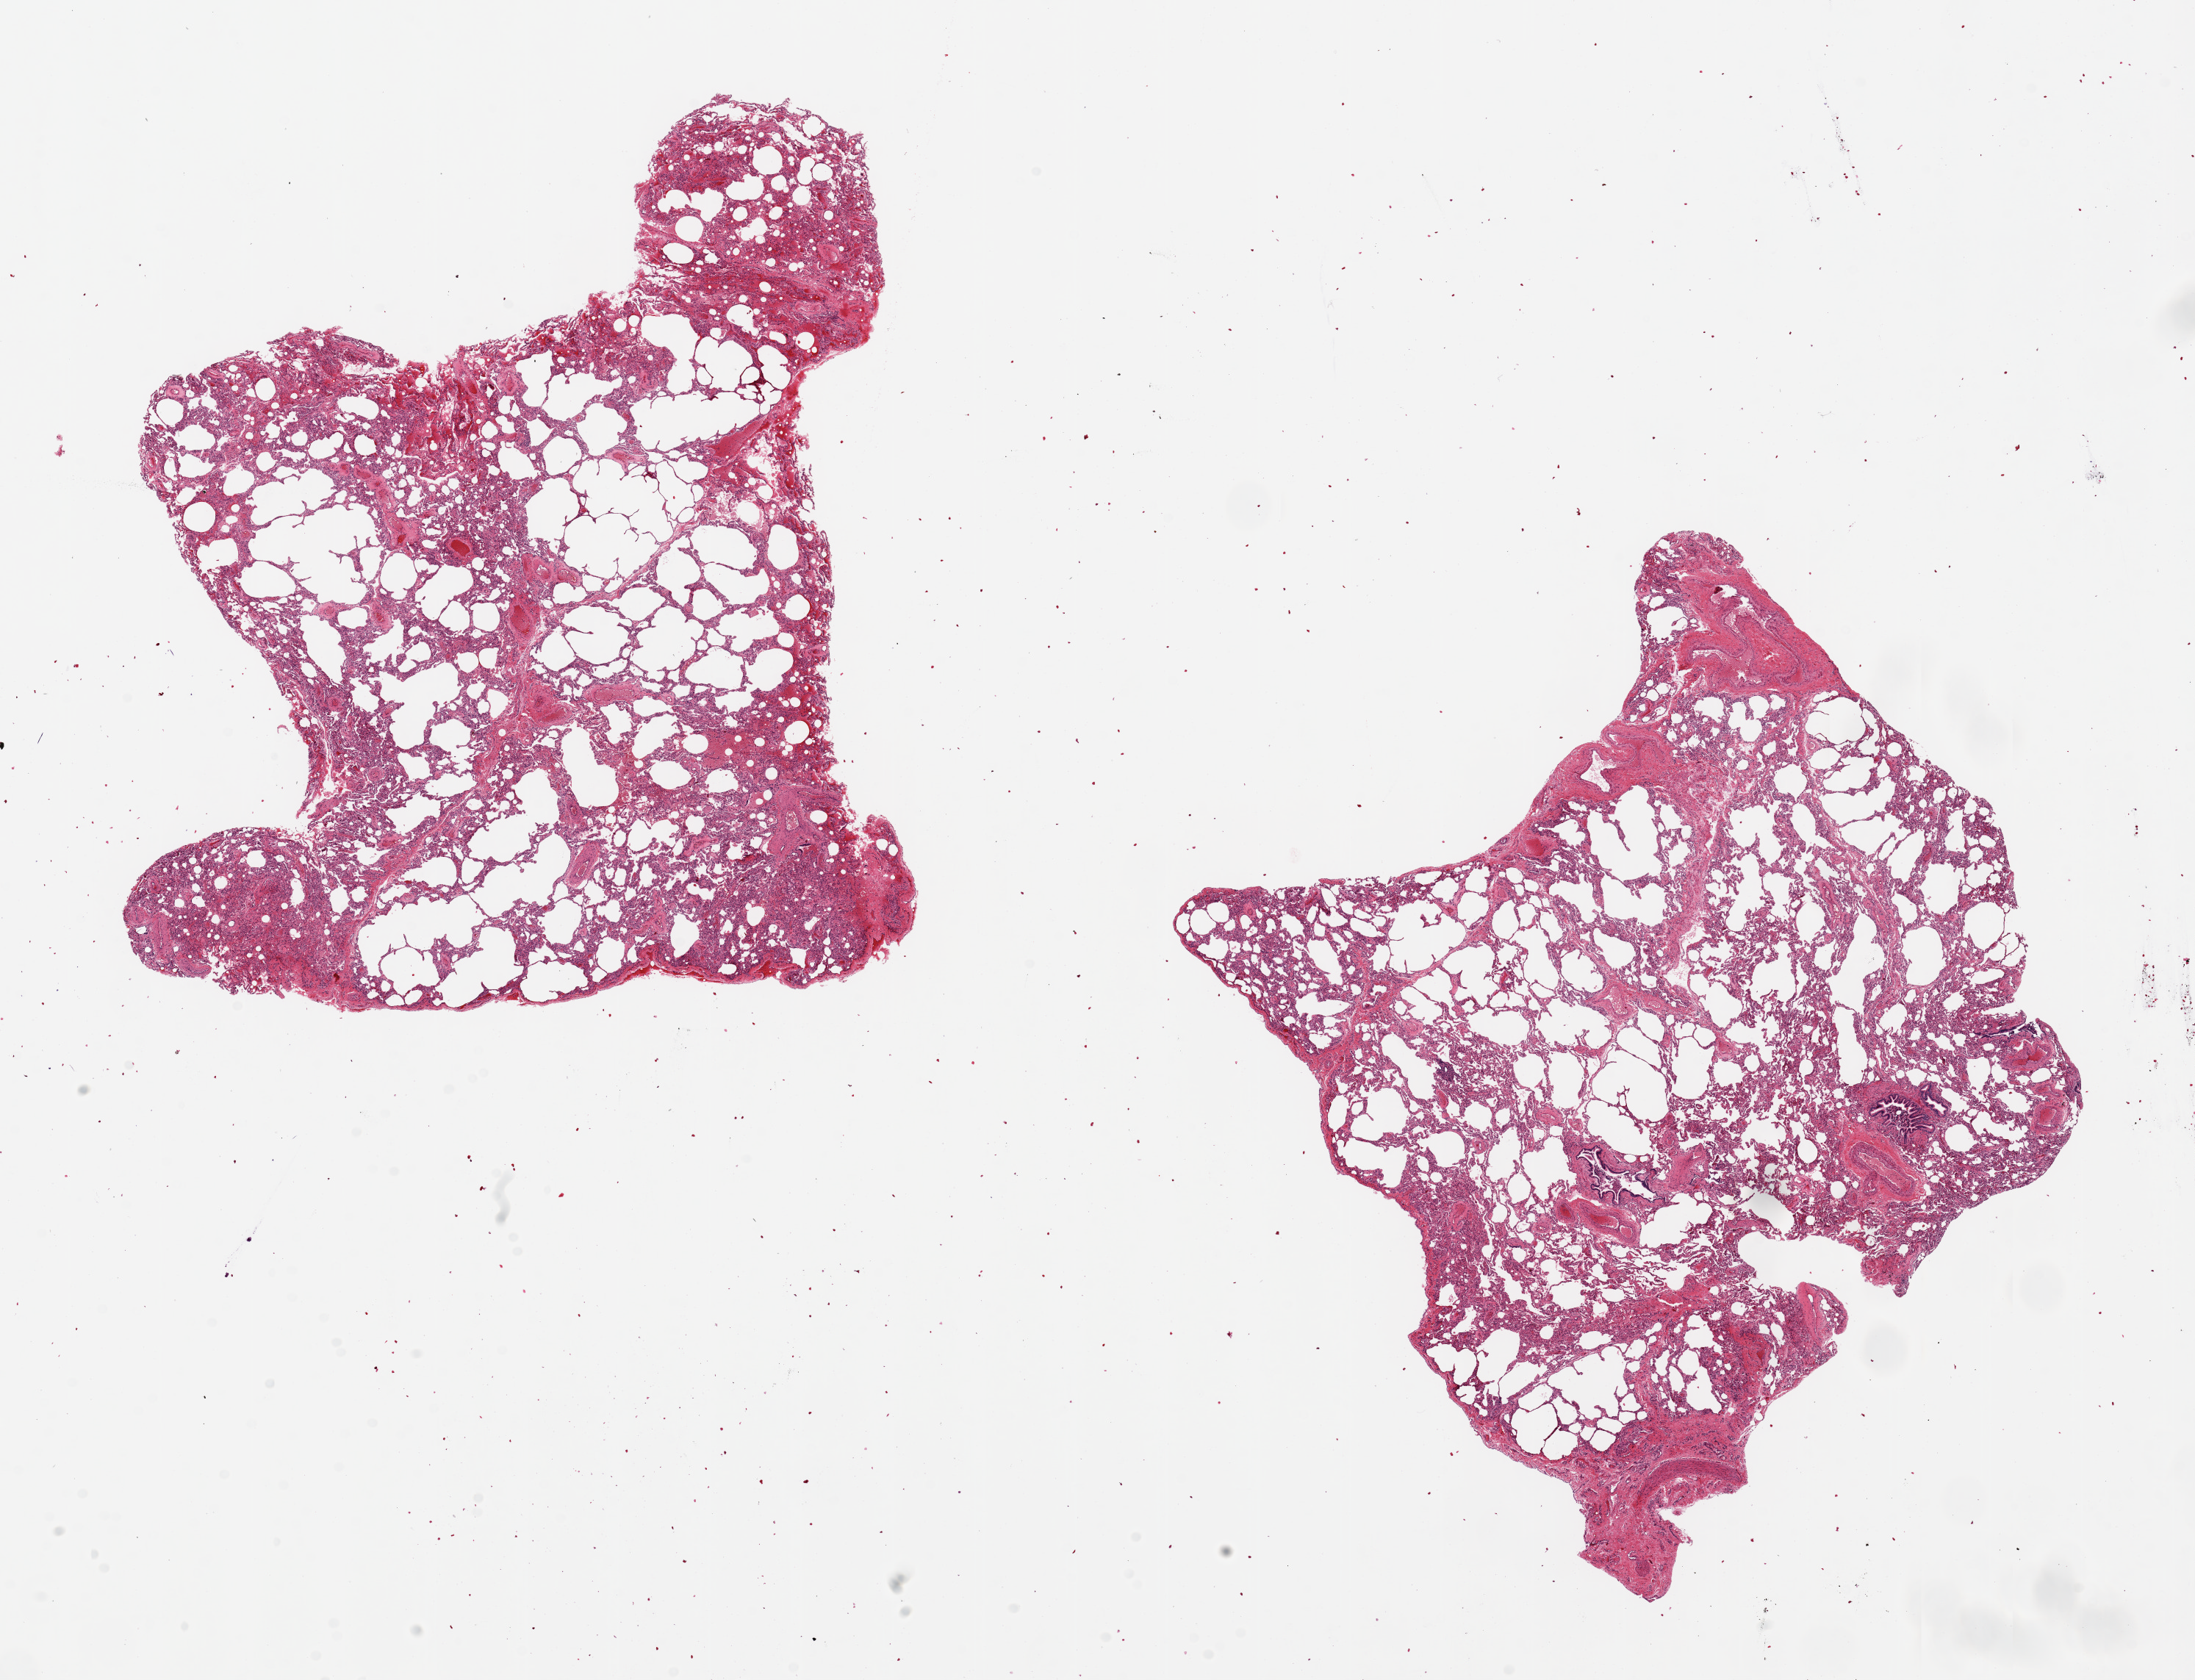
H&E whole-slide image, low-resolution overview of the scanned area, about 23.6 x 18.1 mm (from a 20x scan), PAXgene-fixed, paraffin-embedded tissue, section of lung (target tissue), tissue donor sample. Female donor.
Pathologist's review note for this sample: 2 pieces ~9x7mm moderate congestion/emphysematous changes; Reprsentative bronchiole ~1mm d., relatively well-preserved mucosal lining.